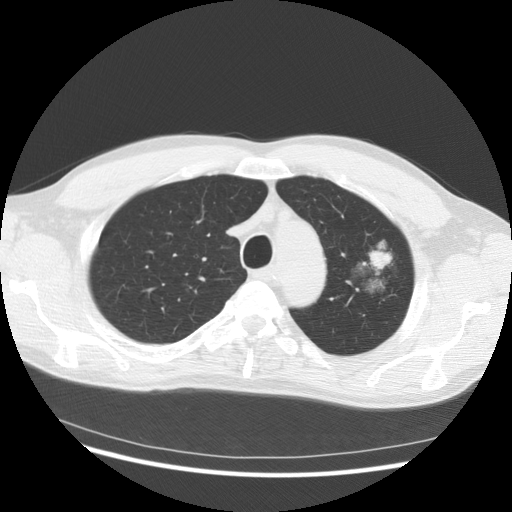
Low-dose screening chest CT, axial slice; third annual screen; lung window (W 1500 / L -600 HU); standard (soft-tissue) reconstruction kernel (STANDARD); 512 × 512 image matrix, field of view 370 × 370 mm. Male participant, aged 61 years at enrolment. Former smoker at enrolment.
- Expert-annotated lung lesion, bounding box <331,238,405,318> (left, top, right, bottom; pixels).
- Screening reader's record for this exam (one nodule recorded; not confirmed to be the boxed lesion): non-calcified nodule or mass ≥4 mm, left upper lobe, 37 × 33 mm, poorly defined margins, mixed attenuation, pre-existing on the prior screen: yes; interval growth: yes.
- Official screen result: positive, other.
- Participant outcome: lung cancer diagnosed 361 days after this screen — bronchiolo-alveolar adenocarcinoma, NOS, left upper lobe, well differentiated (G1), stage IB (AJCC 6th edition), 44 mm at pathology.